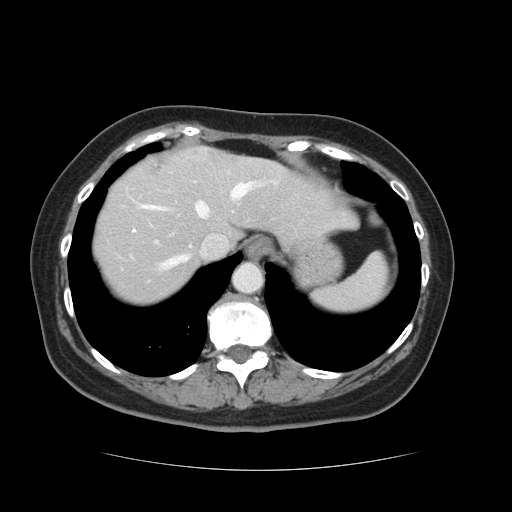
Contrast-enhanced abdominal CT, one axial slice. Slice 105 of 128 in the series (ordered by position). 120 kVp. Soft-tissue window (W 400 / L 40 HU). 2.5 mm slice thickness. 512 × 512 image matrix, field of view 366 × 366 mm. Female patient, age 67 years. Case-level facts recorded for this patient, not image findings: diagnosis: colorectal cancer liver metastases, imaged before liver resection; multiple liver metastases: yes; largest metastasis: 3 cm; disease in both lobes: yes.
Outlined on this slice (manually delineated by an expert):
- hepatic veins: box from (x=130, y=182) to (x=258, y=271) px
- liver: (x=92, y=147)–(x=352, y=305)
- planned liver remnant (the part of the liver to remain after resection): (x=92, y=158)–(x=353, y=305)
- liver metastasis: (x=146, y=161)–(x=162, y=179)